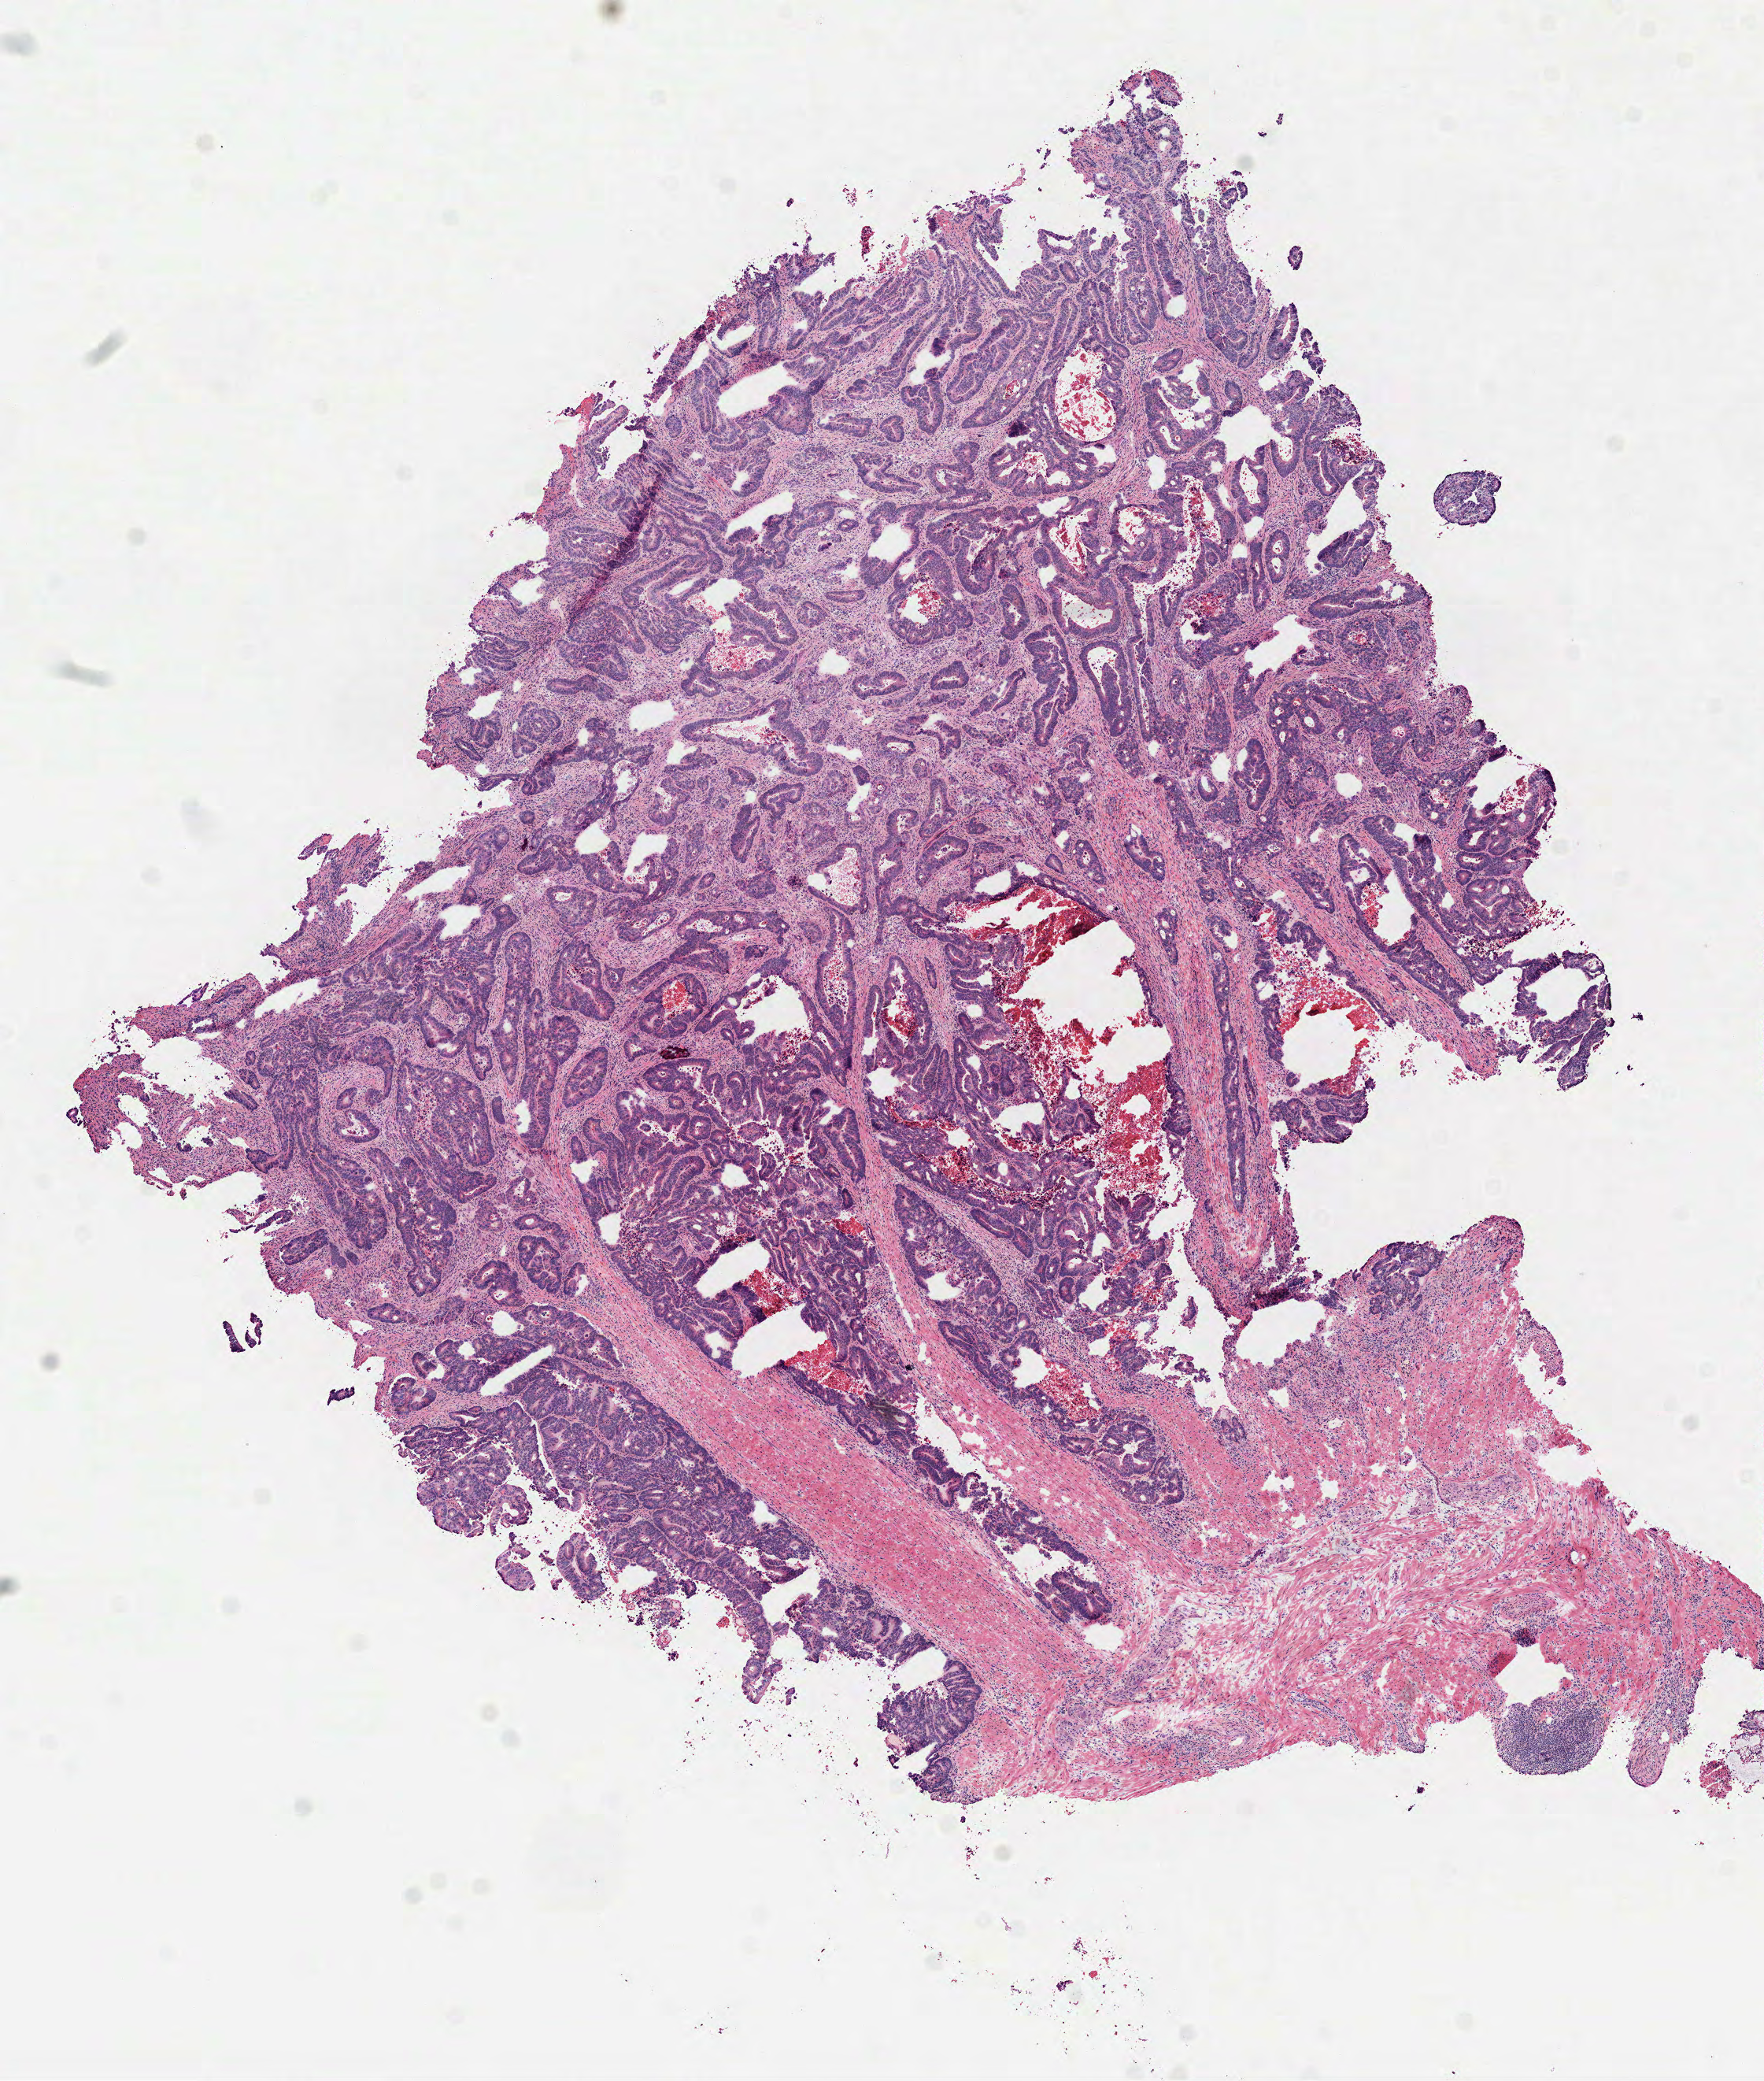
Whole-slide histology image, H&E-stained, whole scanned area (about 9.0 x 10.7 mm, slide scanned at 40x) shown as a low-resolution overview, frozen section, rectum, primary tumour sample. Male, age 43 years at initial diagnosis. Pathologist review of this section (percent, as recorded): tumour cells 75%, tumour nuclei 80%.
Histologic diagnosis: Adenocarcinoma, NOS.